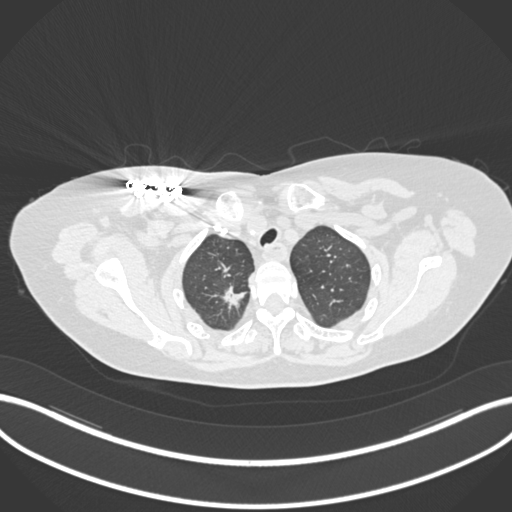
Chest CT, one axial slice. Slice 153 of 176 in the series (ordered by position). Reconstruction kernel B30f. 120 kVp. Lung window (W 1500 / L -600 HU). 512 × 512 image matrix, field of view 400 × 400 mm. Female patient, age 72 years. Case-level facts recorded for this patient, not image findings: clinical TNM (as recorded): T1c N0 M0.
Structures marked on this image (bounding box drawn by a radiologist):
- lung tumour (recorded histology: adenocarcinoma): bounding box [x1, y1, x2, y2] px = [219, 280, 248, 312]